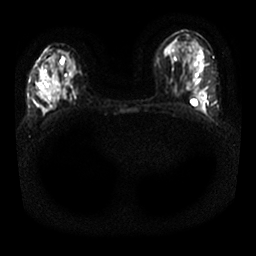
Breast MRI, one axial slice; position 11 of 25 along the scan axis; diffusion-weighted series; image 2 of 4 stored at this slice position (different b-values; order by instance number); 1.5 T; 256 × 256 image matrix. Female patient.
Structures marked on this image (expert manual segmentation):
- tumour on diffusion-weighted imaging: bounding box <63,89,69,98> (left, top, right, bottom; pixels)